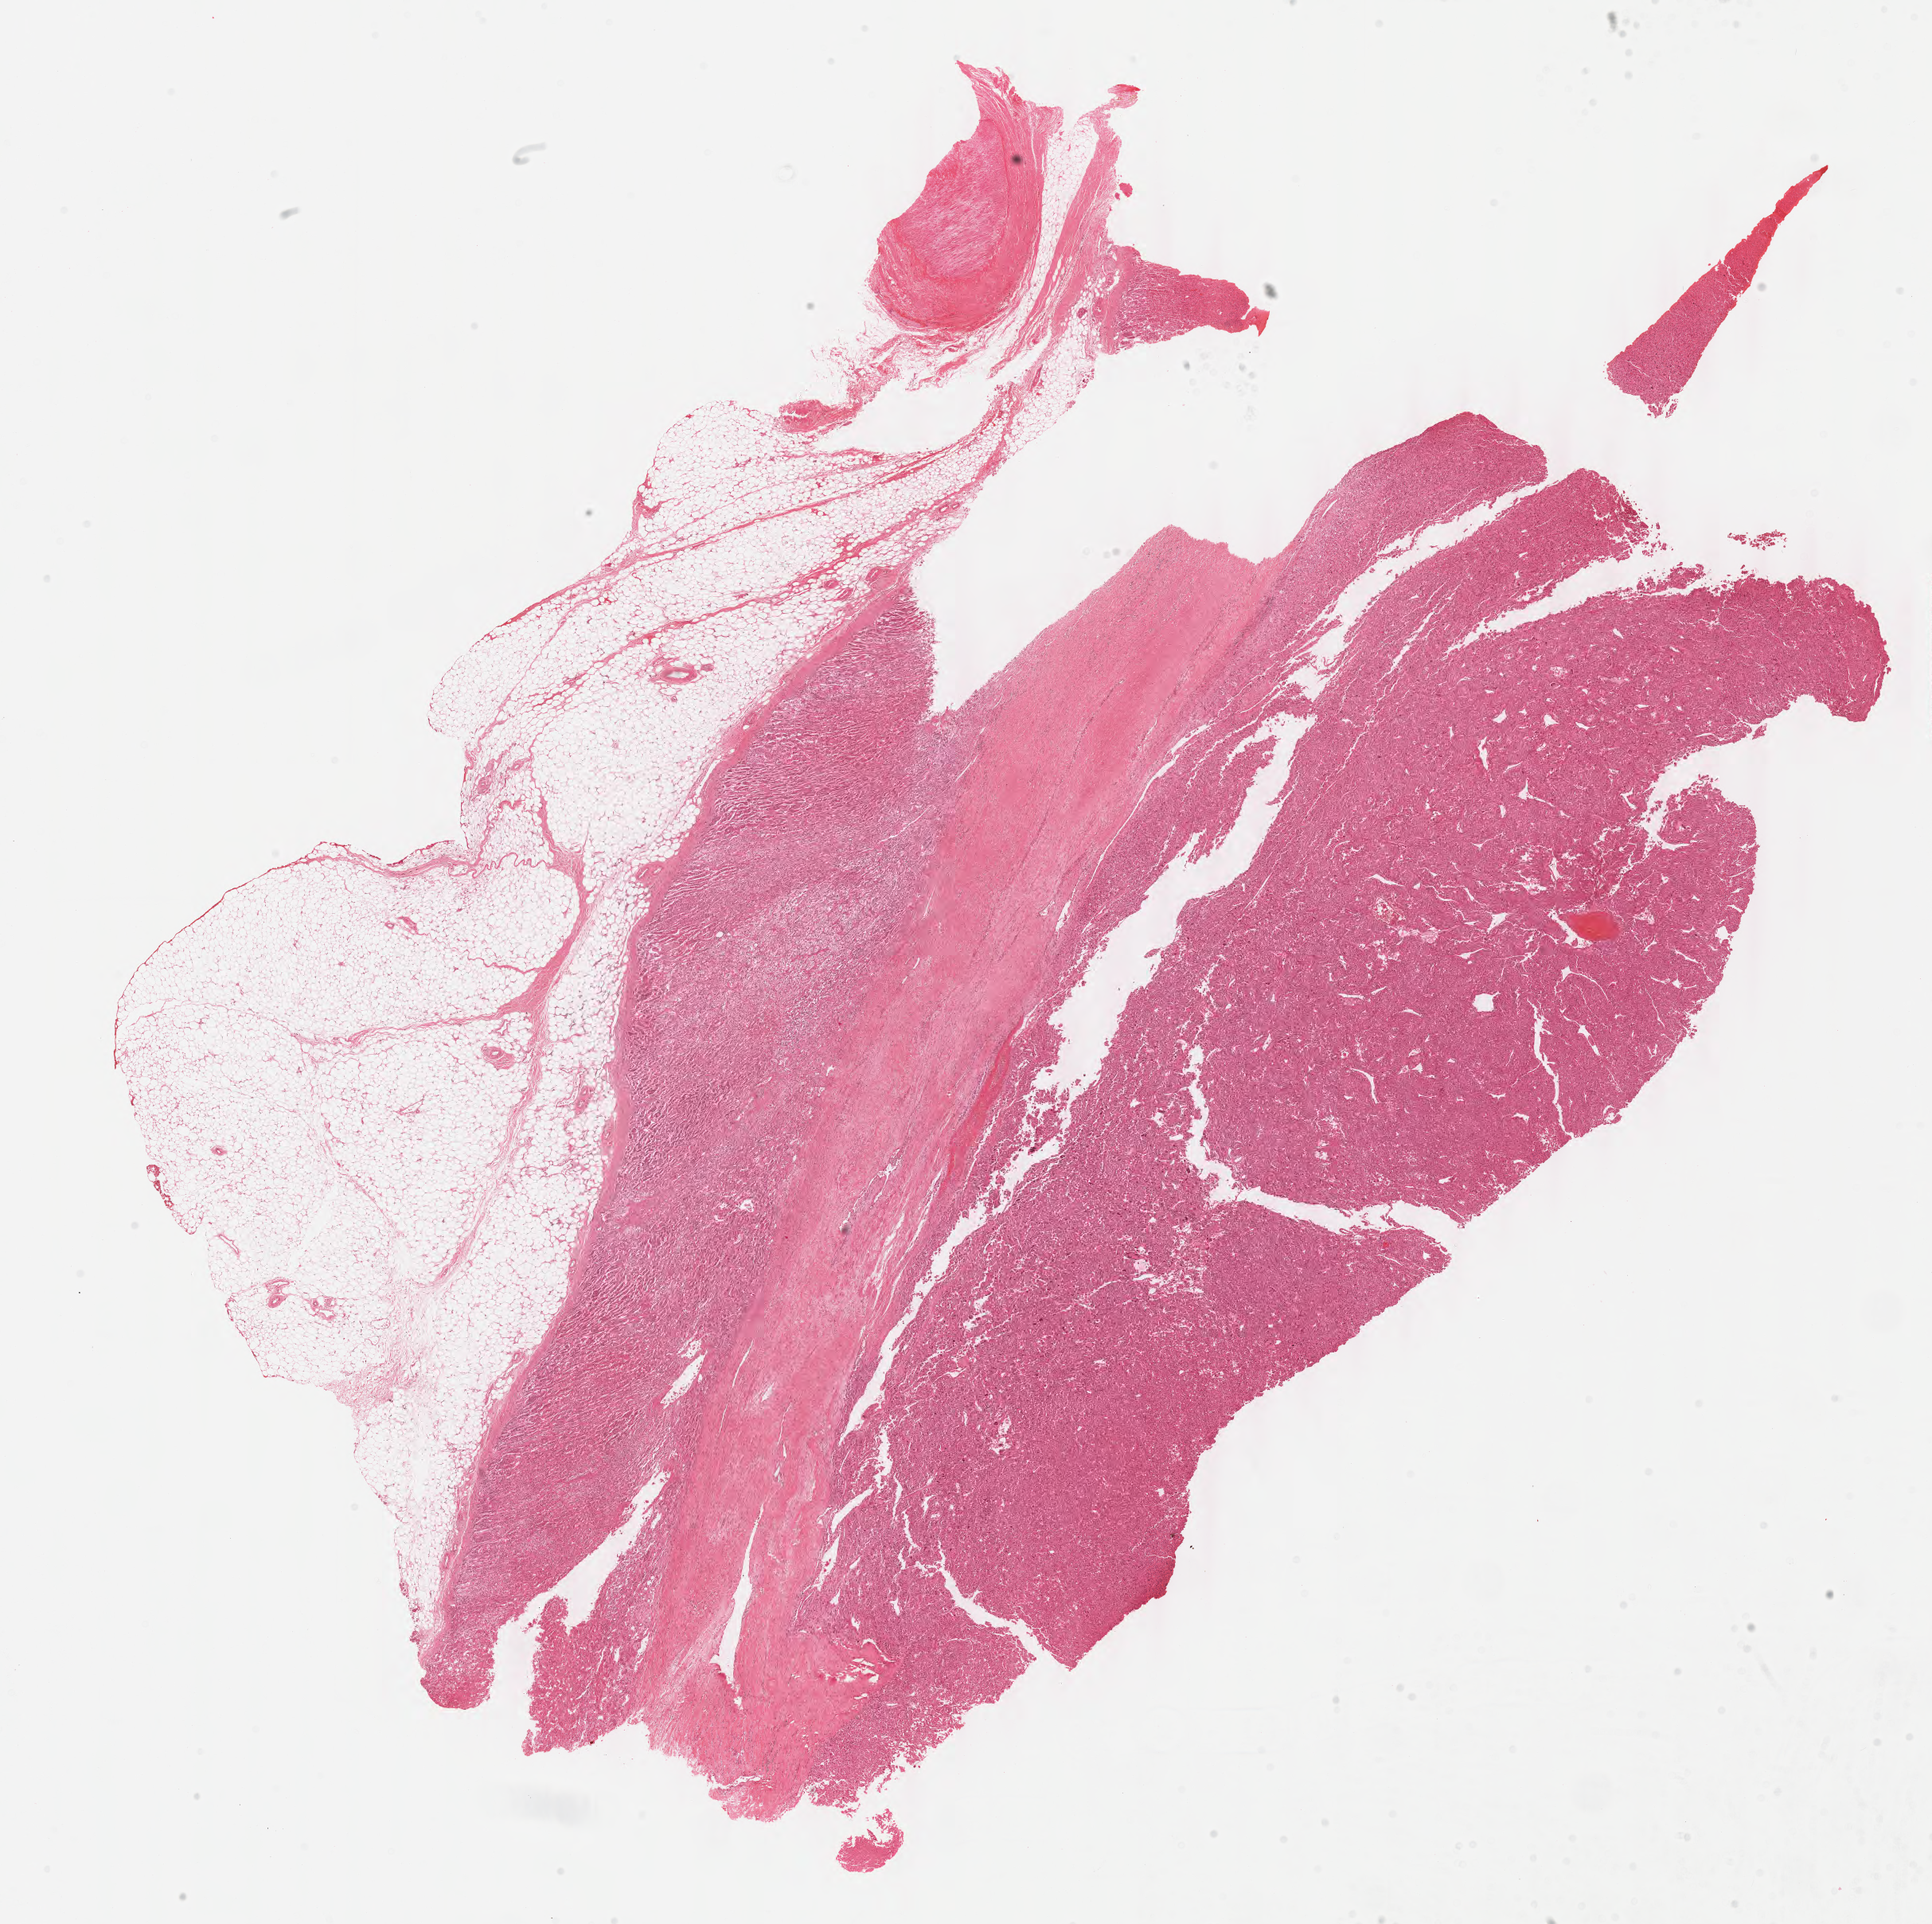
Whole-slide histology image, H&E-stained — a low-resolution overview of the entire scanned area, about 19.2 x 19.1 mm (from a 40x scan), formalin-fixed paraffin-embedded (FFPE) diagnostic section, sample: primary tumour, adrenal cortex. Male patient; age at initial diagnosis 63 years.
Histologic diagnosis: Adrenal cortical carcinoma (cortex of adrenal gland).